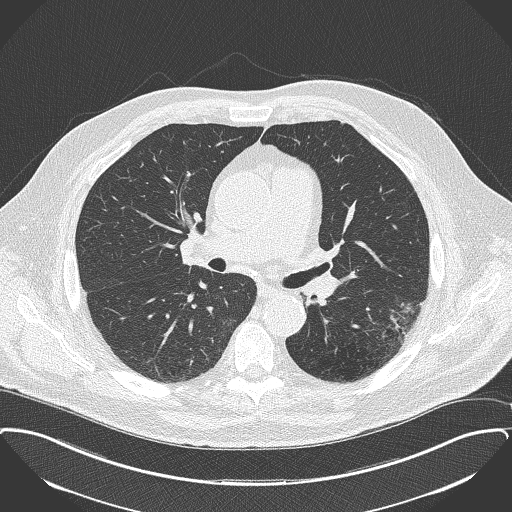
Low-dose screening chest CT, axial slice; second annual screen; lung window (W 1500 / L -600 HU); 2 mm slice thickness; 120 kVp; slice 75 of 175 in the series. Male participant, aged 68 years at enrolment. Former smoker at enrolment.
- Lesion marked by an expert reader, bounding box [x1, y1, x2, y2] px = [373, 293, 430, 346].
- The screening reader recorded 2 non-calcified nodules or masses ≥4 mm on this exam (left lower lobe, left lower lobe); which of them this box marks is not recorded.